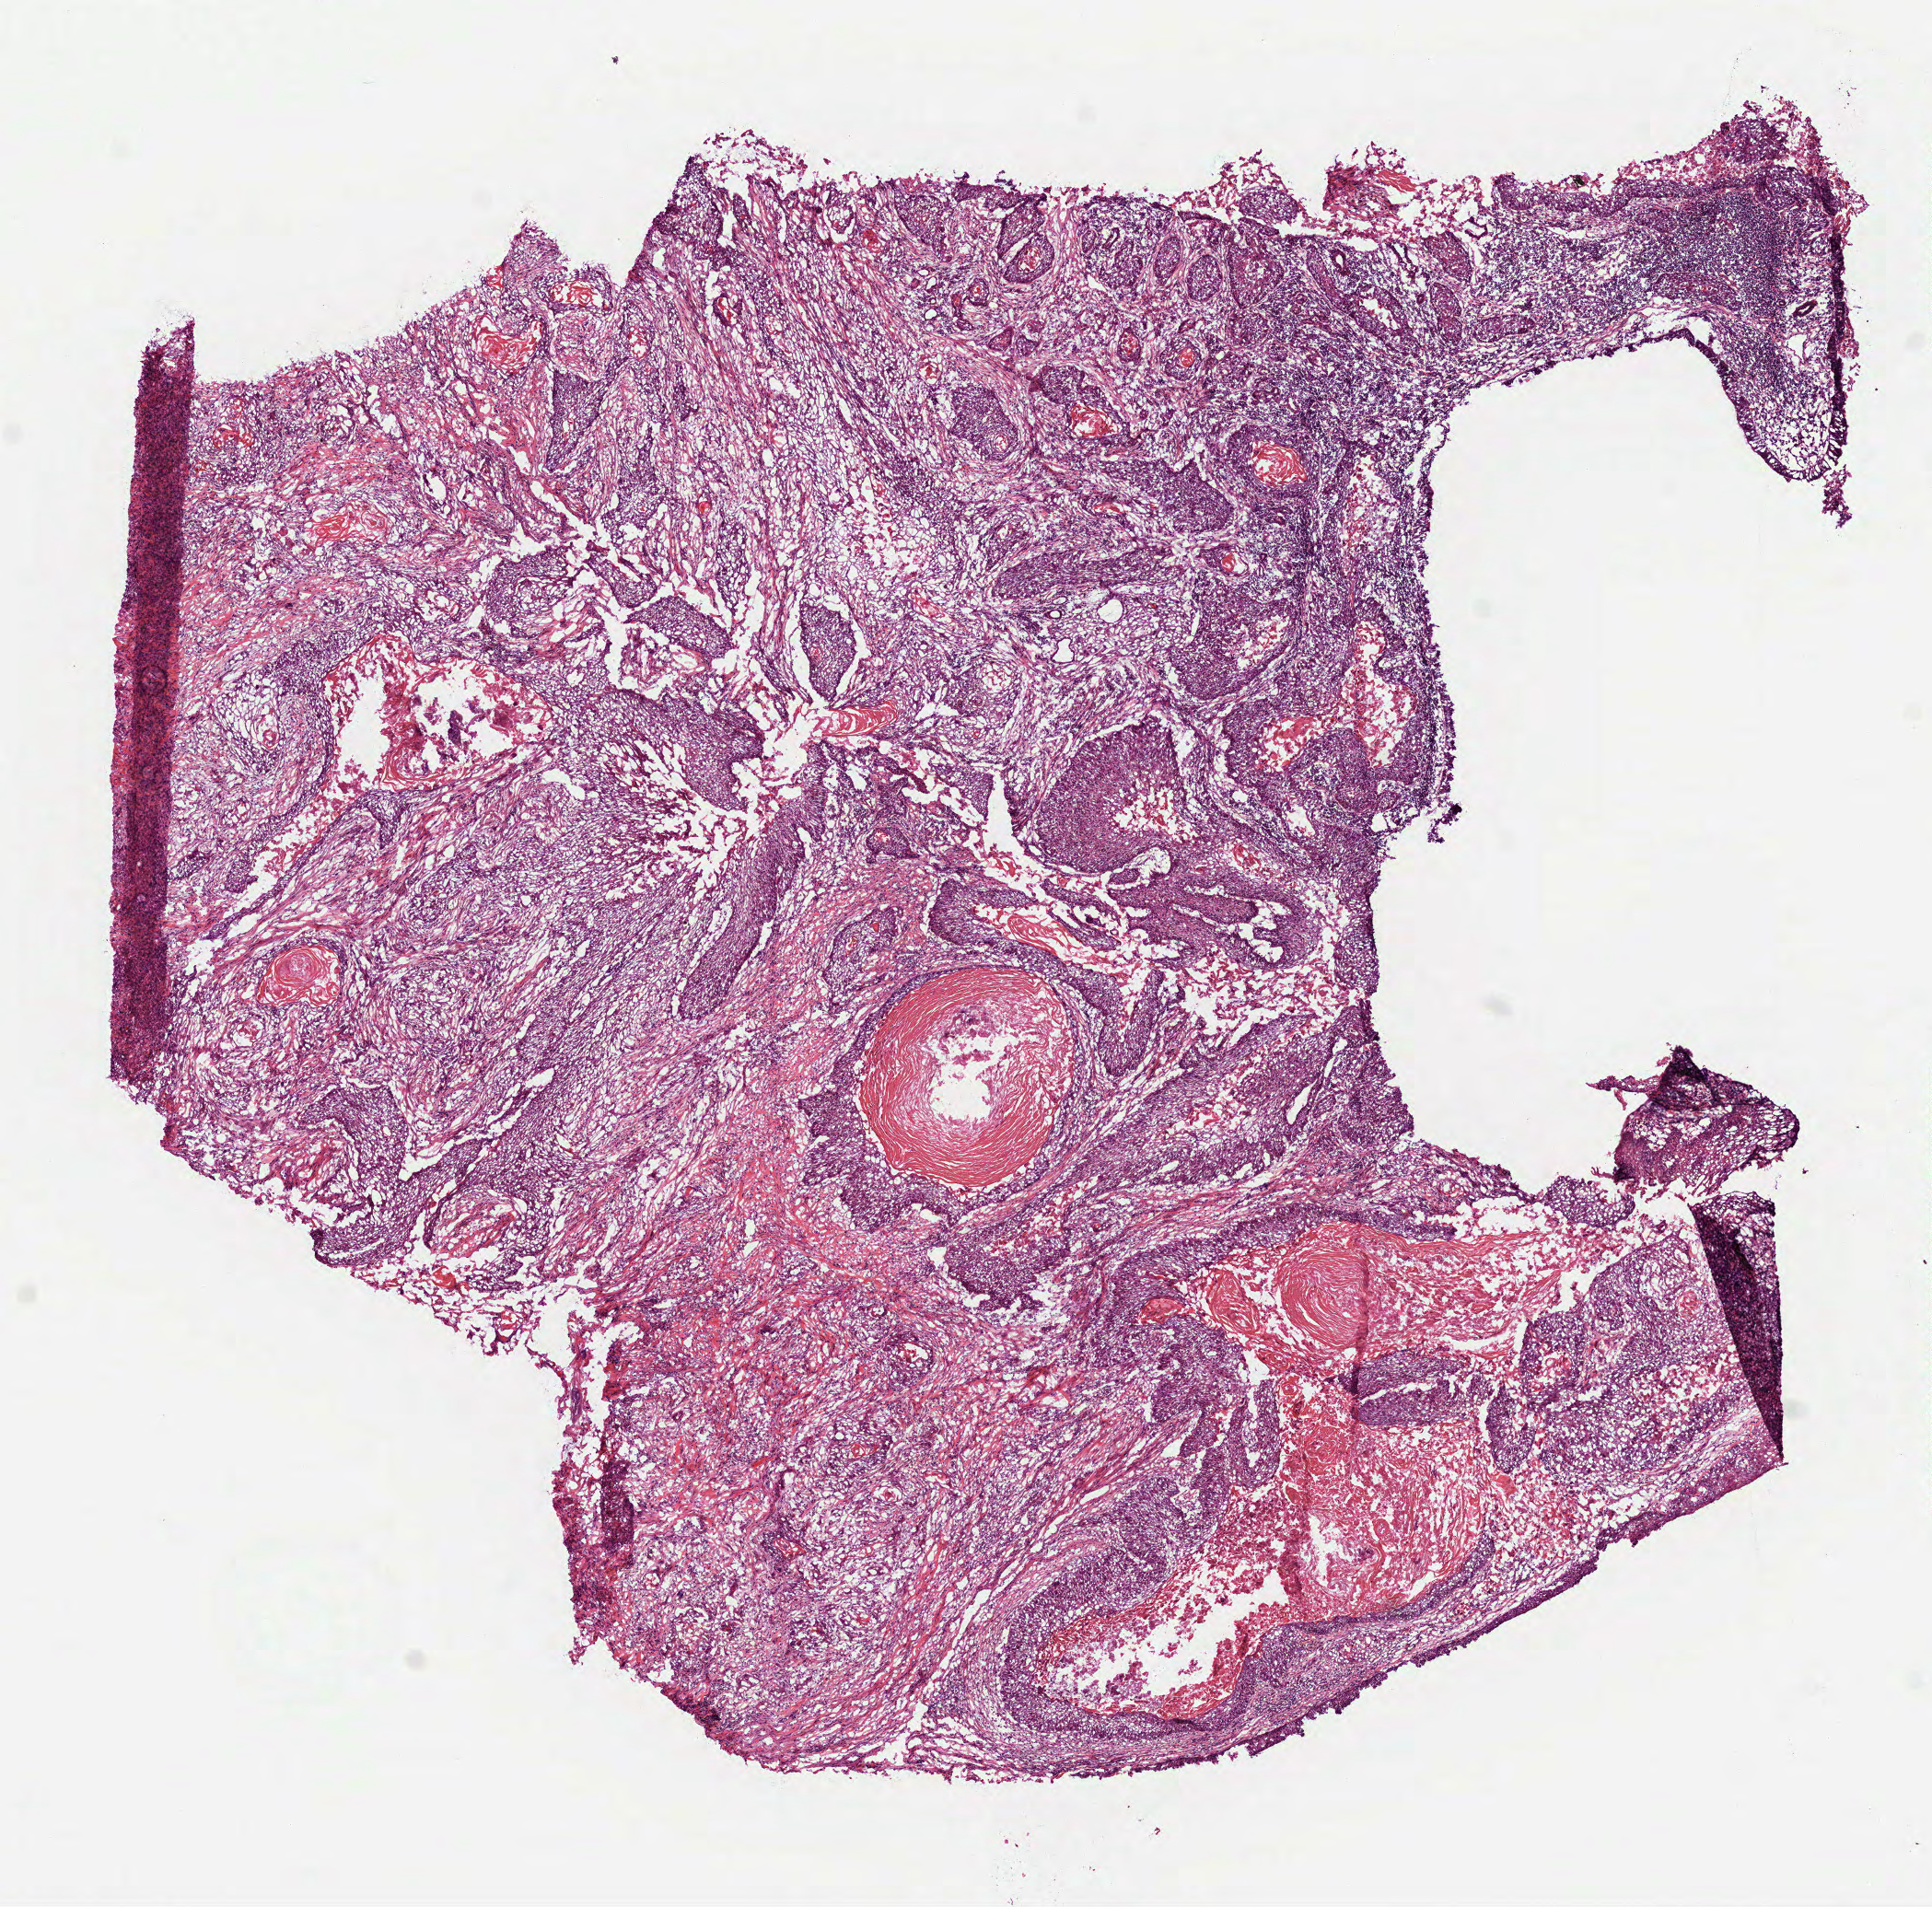
Whole-slide histology image, H&E — shown as a low-resolution overview of the whole scanned area (about 8.5 x 8.4 mm). Frozen section from the bottom of the tissue portion. Sample: primary tumour, head and neck. Female, age 60 years at initial diagnosis. Histologic grade: G2 (moderately differentiated). Pathologist review of this section (percent, as recorded): tumour cells 85%, tumour nuclei 75%, normal cells 0%, stromal cells 15%, necrosis 0%.
- AJCC pathologic stage: II (7th edition)
- histologic diagnosis: Squamous cell carcinoma, NOS